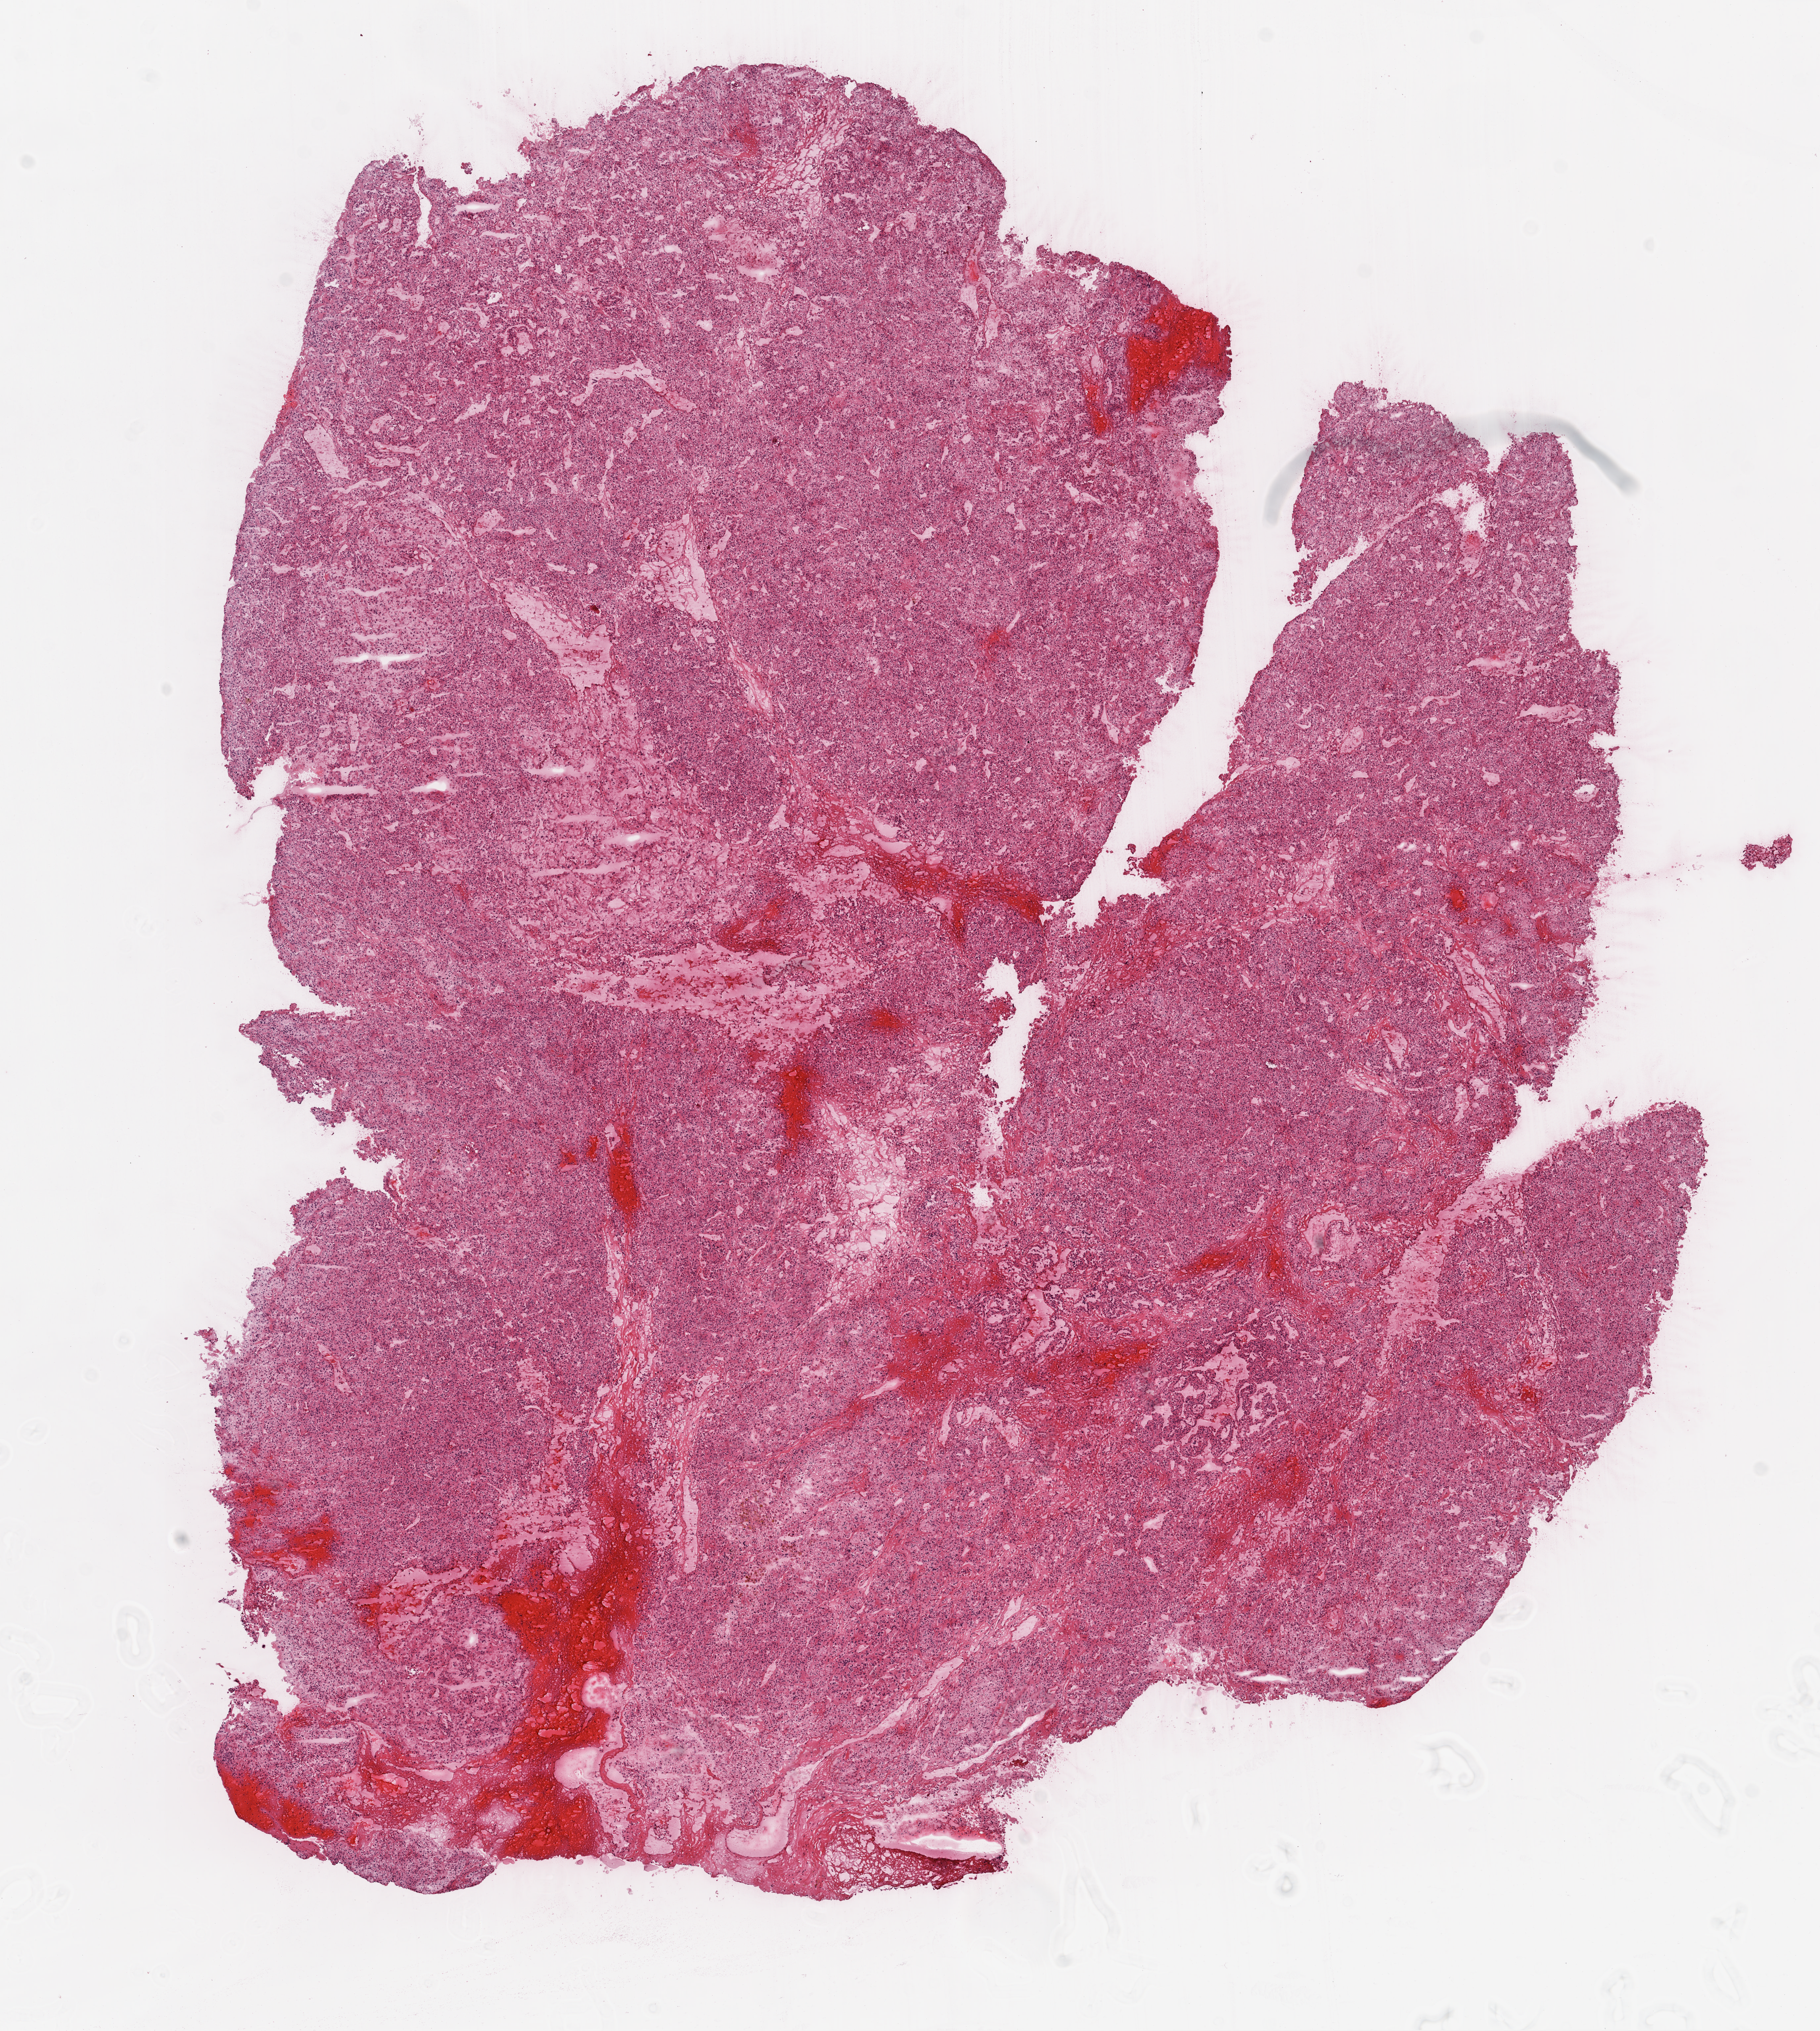
Whole-slide histology image, H&E-stained, shown as a low-resolution overview of the whole scanned area (about 11.0 x 12.3 mm, from a 20x scan); frozen section from the top of the tissue portion; sample: primary tumour, kidney. Patient: male, age at initial diagnosis 57 years.
Histologic diagnosis: Clear cell adenocarcinoma, NOS.